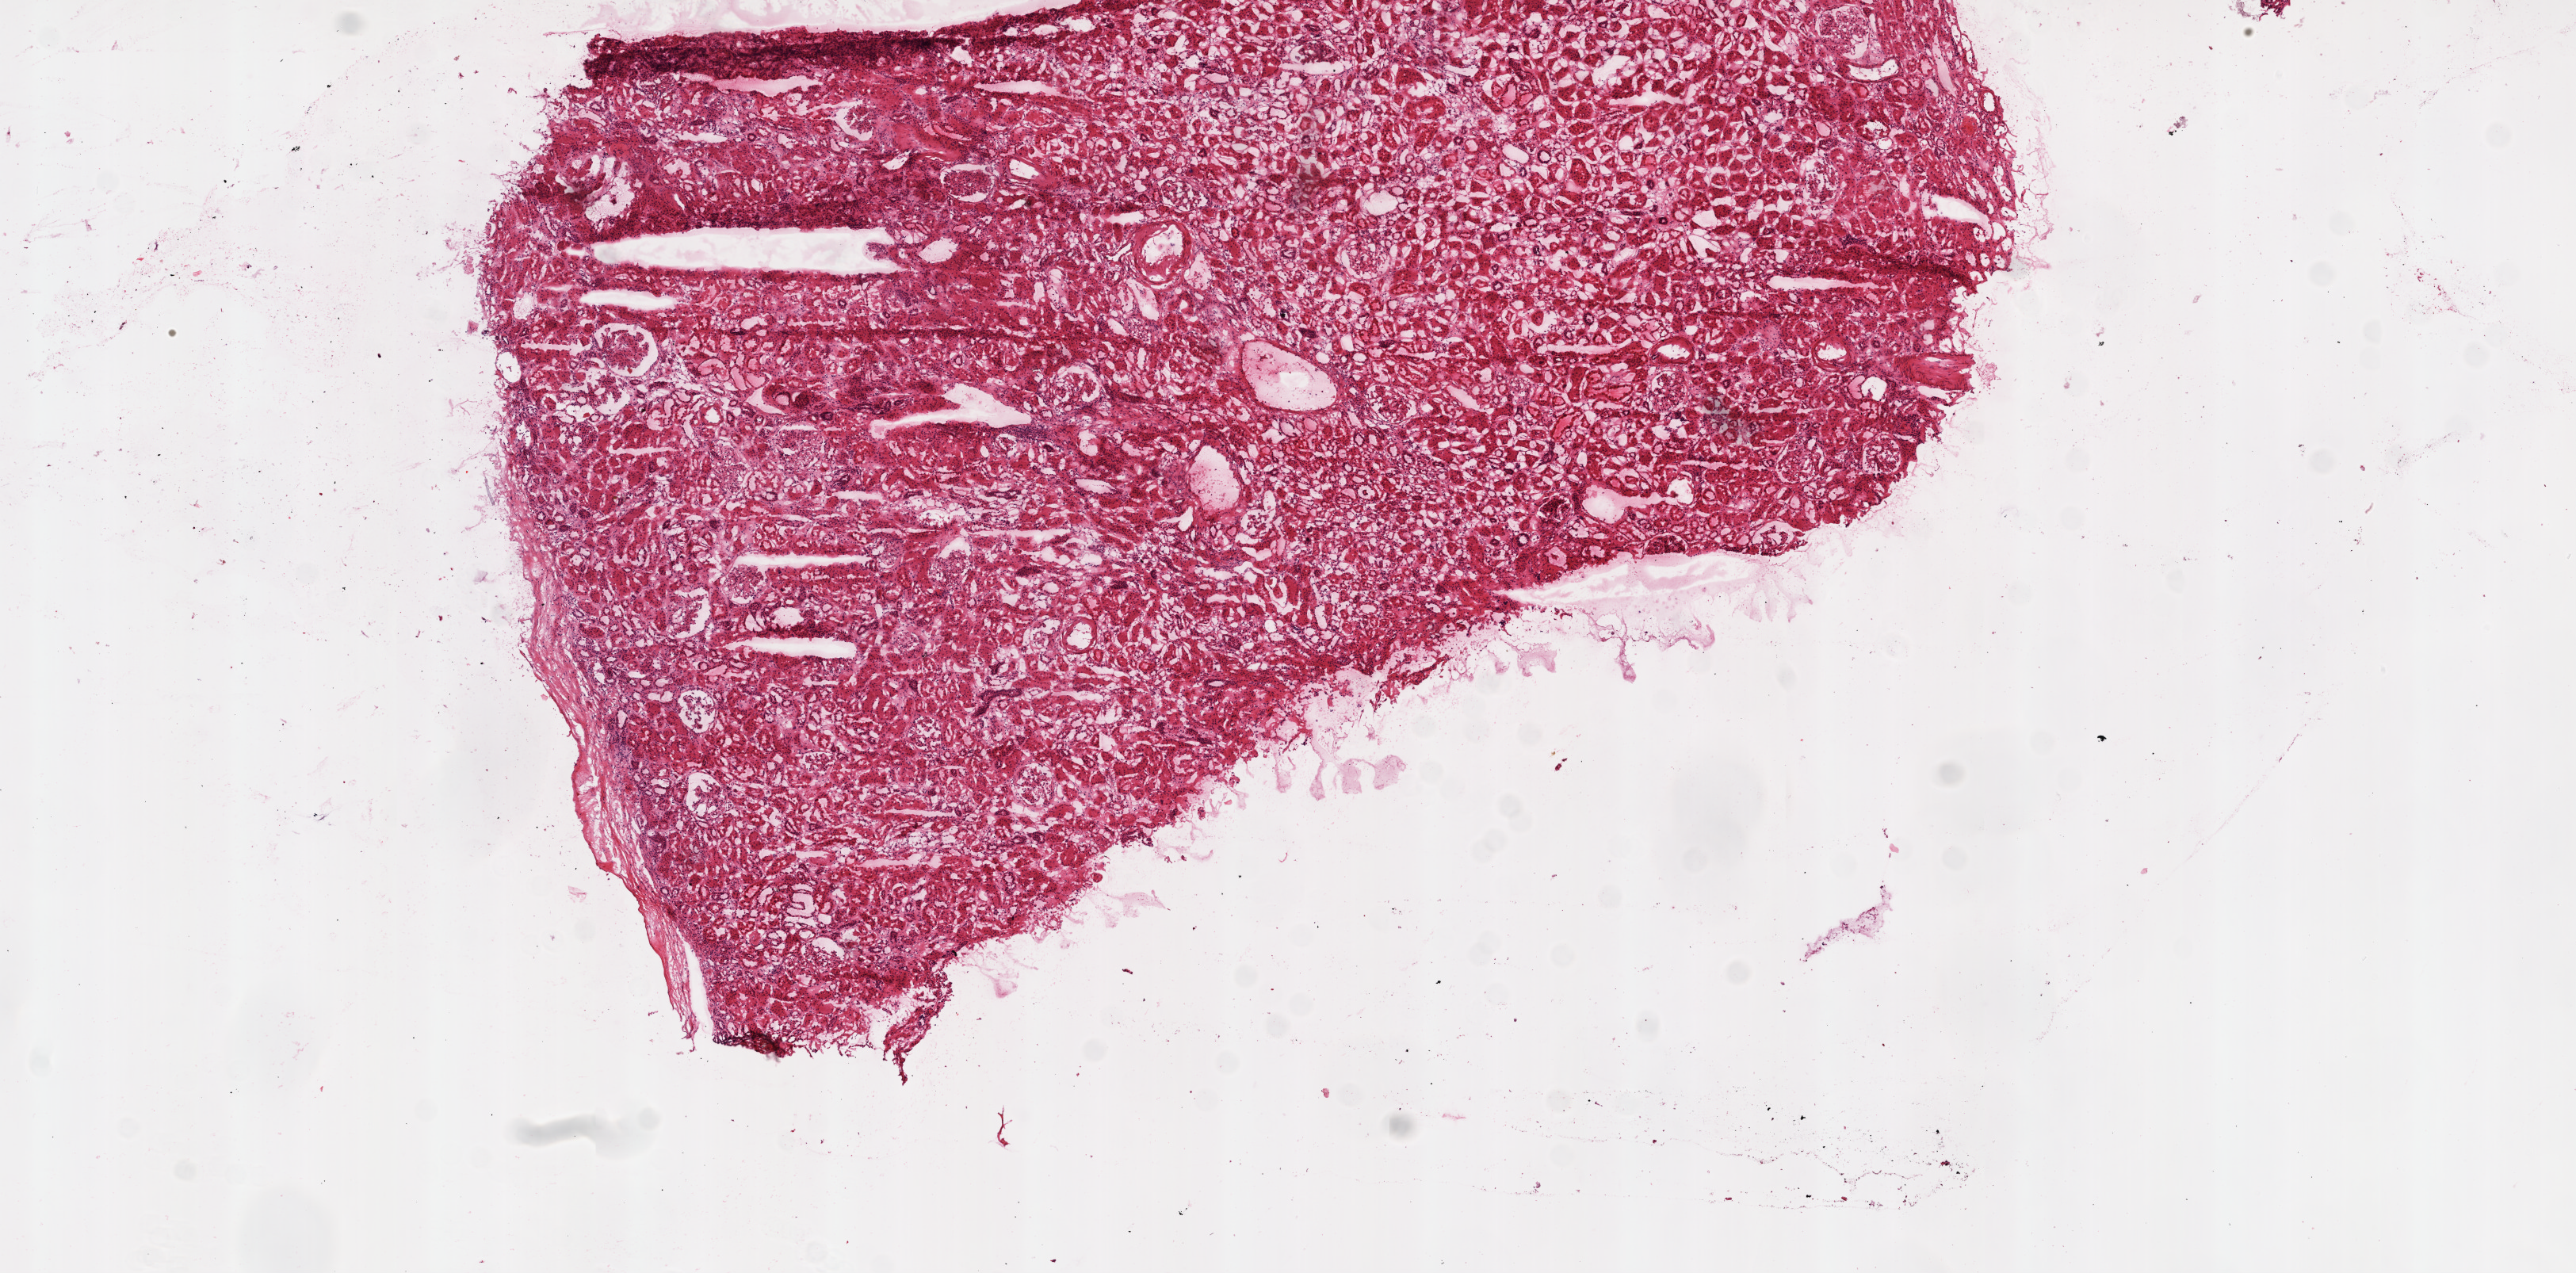
Whole-slide histology image, H&E-stained — whole scanned area (about 13.0 x 6.4 mm, slide scanned at 20x) shown as a low-resolution overview. Frozen section from the top of the tissue portion. Sample: solid tissue normal (non-tumour tissue), kidney. Female, age 59 years at initial diagnosis.
This section: solid tissue normal (non-tumour) sample from the same patient. Patient diagnosis: Clear cell adenocarcinoma, NOS.